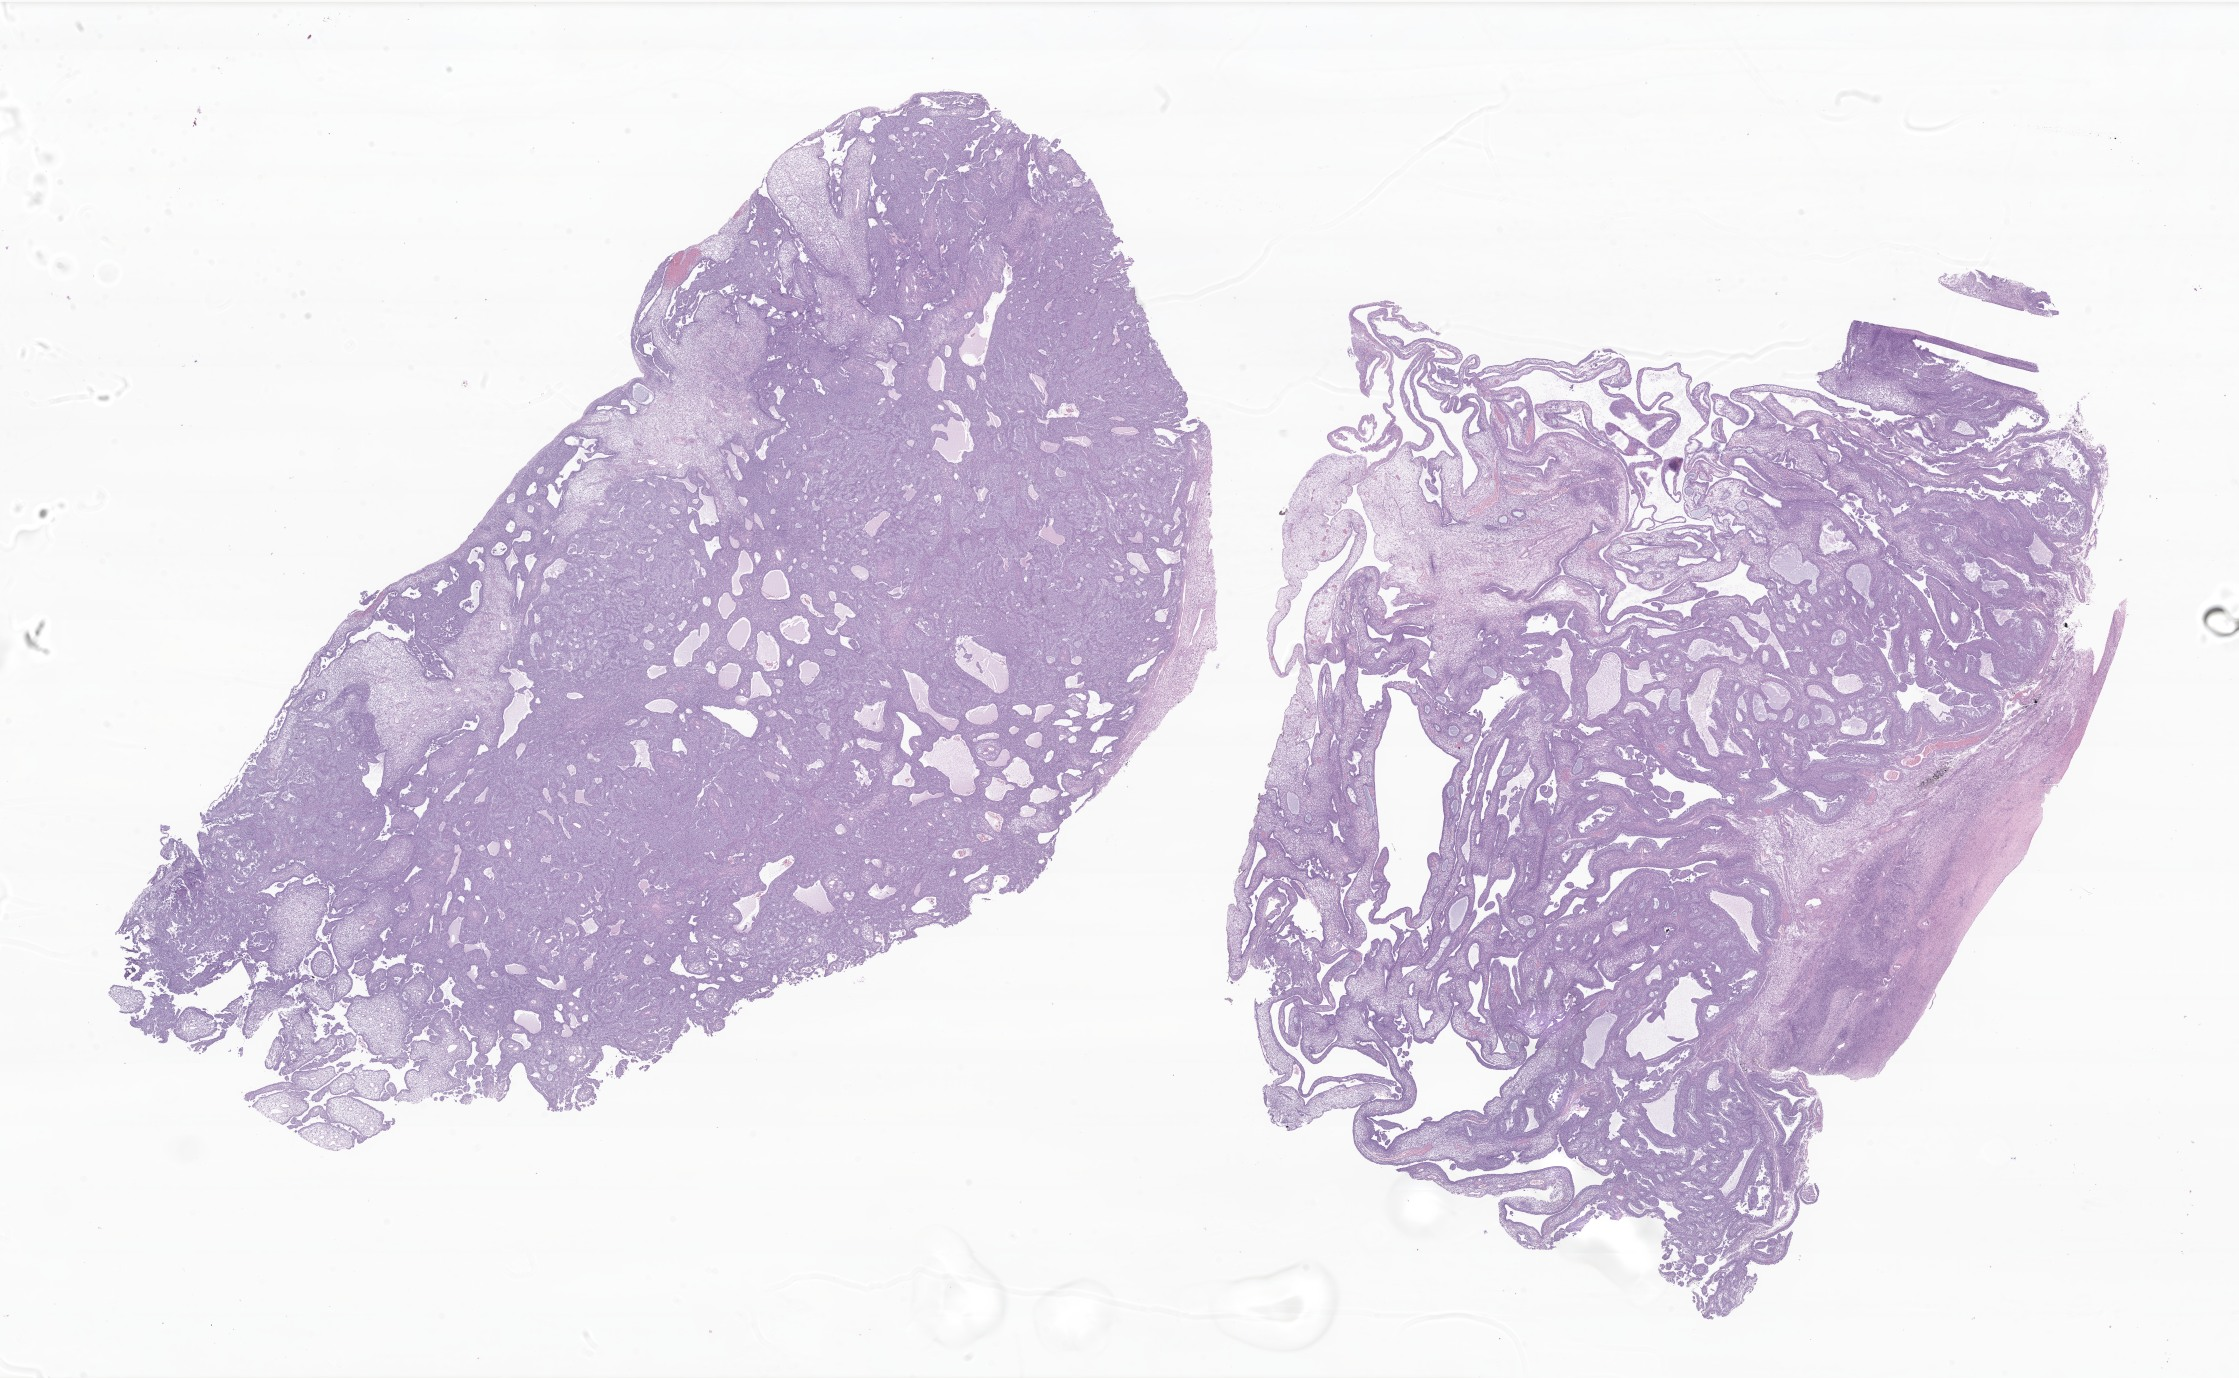
Whole-slide image, haematoxylin and eosin stain of tumor tissue from the ovary — whole scanned area (about 37.8 x 23.2 mm) shown as a low-resolution overview, FFPE section. Patient female; age 168 months (14 years).
• diagnosis (ICD-O-3 morphology term): Granulosa cell tumor, juvenile